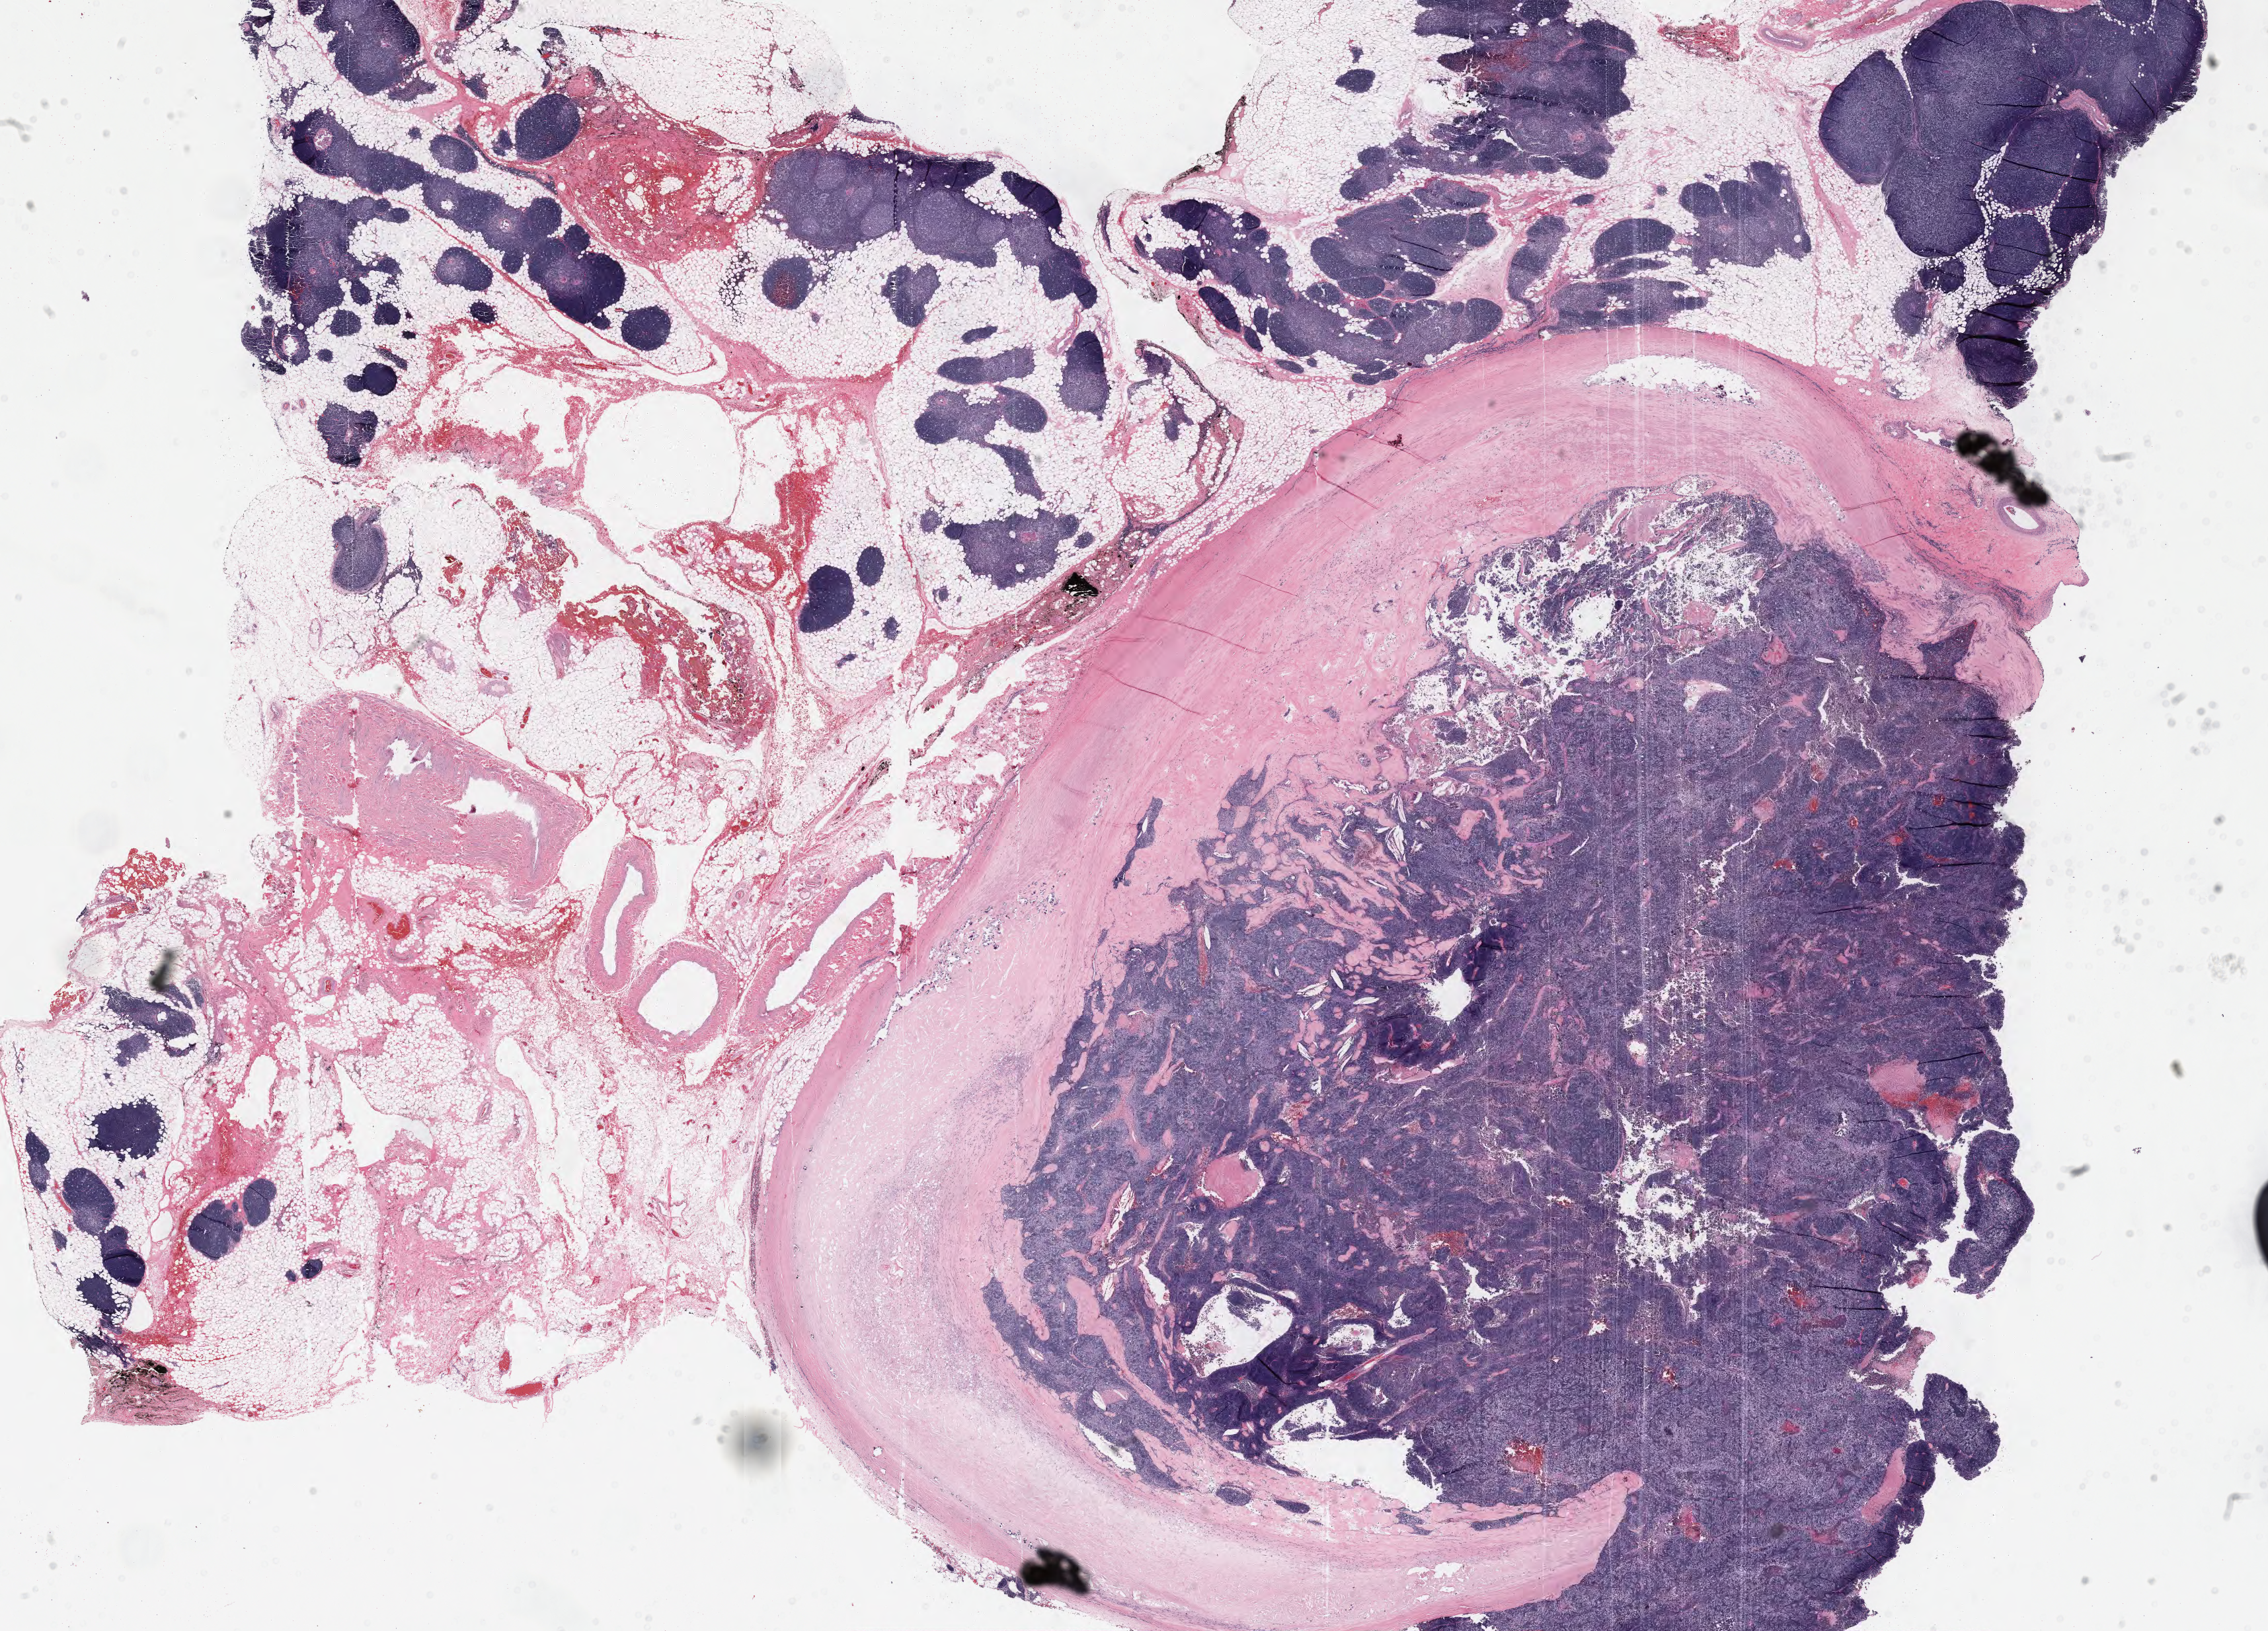
Whole-slide histology image, H&E-stained — shown as a low-resolution overview of the whole scanned area (about 27.2 x 19.6 mm, from a 40x scan); formalin-fixed paraffin-embedded (FFPE) diagnostic section; primary tumour sample from the thymus. Male, age 44 years at initial diagnosis.
Diagnosis: Thymoma, type B2, malignant.